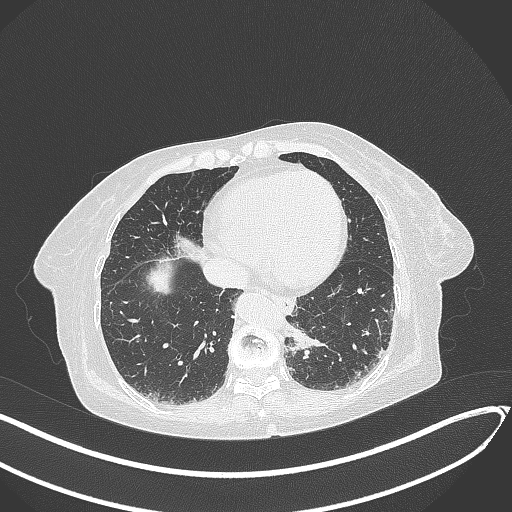
Chest CT, one axial slice. Position 59 of 324 along the scan axis. Reconstruction kernel B70f. 120 kVp. Lung window (W 1500 / L -600 HU). 1 mm slice thickness. 512 × 512 image matrix, field of view 400 × 400 mm. Female patient, age 82 years. Case-level facts recorded for this patient, not image findings: clinical TNM (as recorded): T1b N0 M1.
Annotated regions visible in this slice (rectangle marked by the reading radiologist):
- lung tumour (recorded histology: adenocarcinoma): bounding box (x1, y1, x2, y2) in pixels: (285, 325, 333, 360)